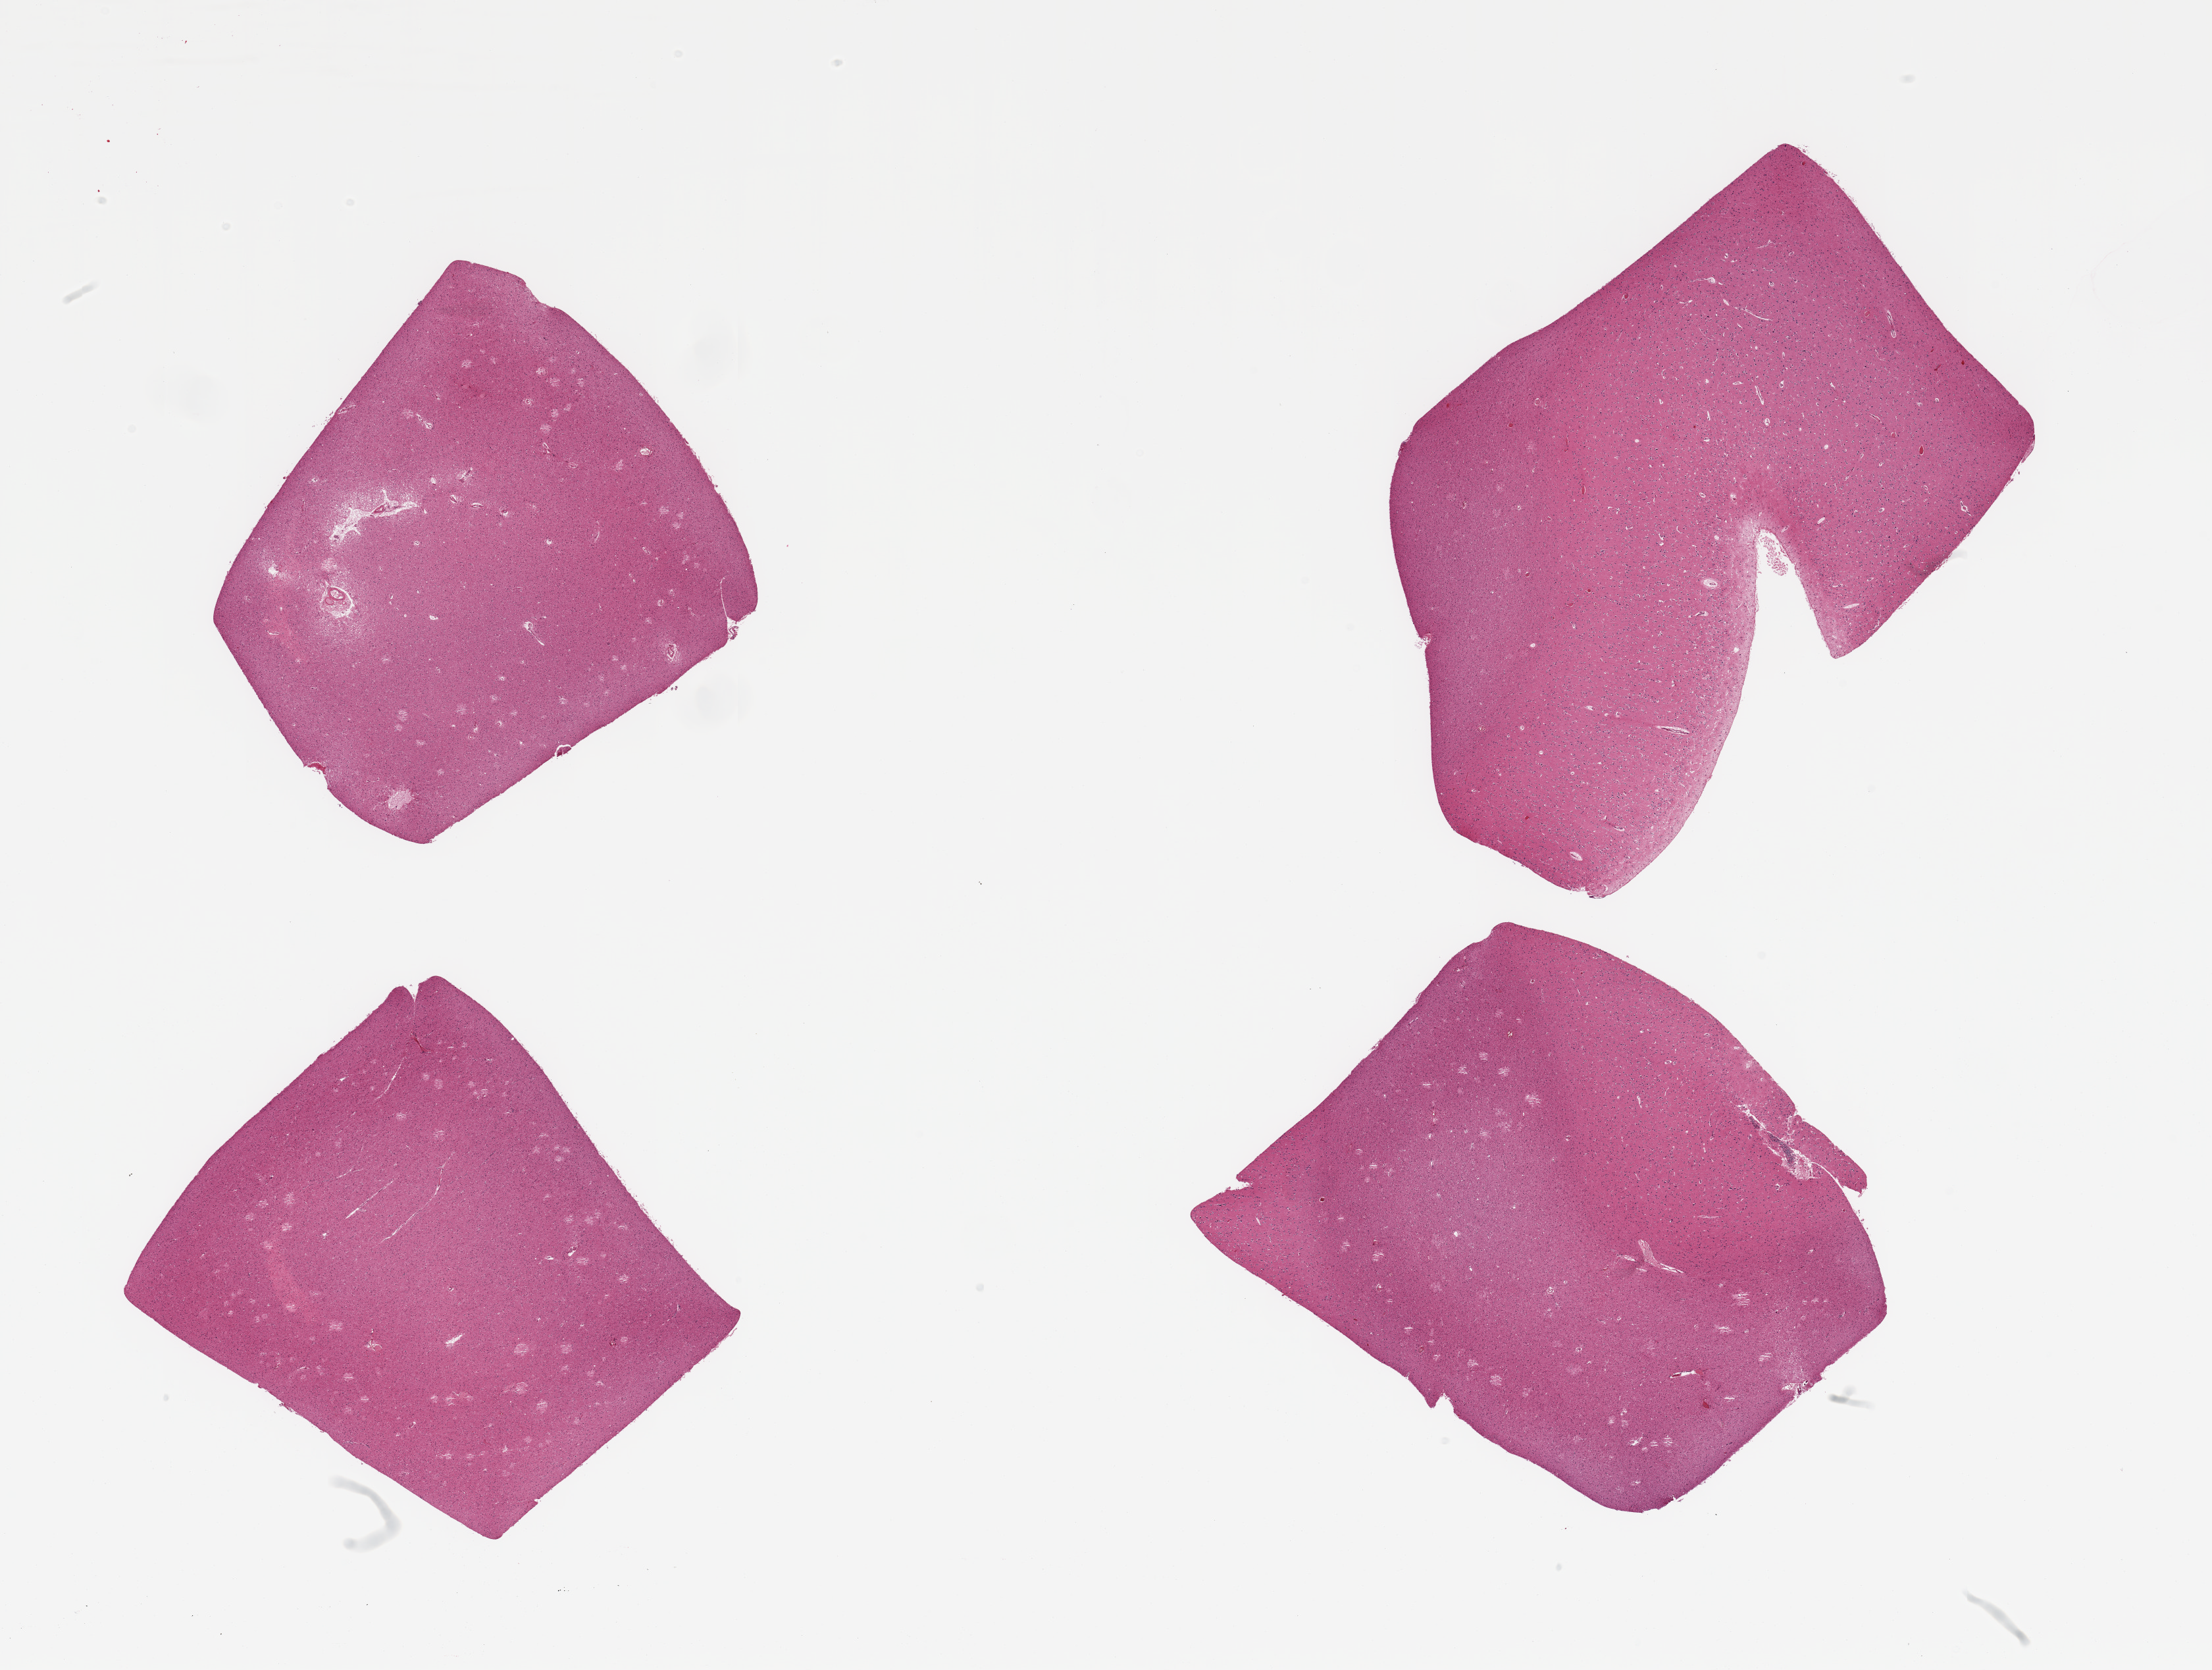
Digitized H&E-stained section, brightfield — whole scanned area (about 26.6 x 20.1 mm) shown as a low-resolution overview. PAXgene-fixed, paraffin-embedded tissue. Section of cerebral cortex (target tissue). Tissue donor sample. Donor sex: male.
Reviewer comment on this tissue sample: 4 pieces.